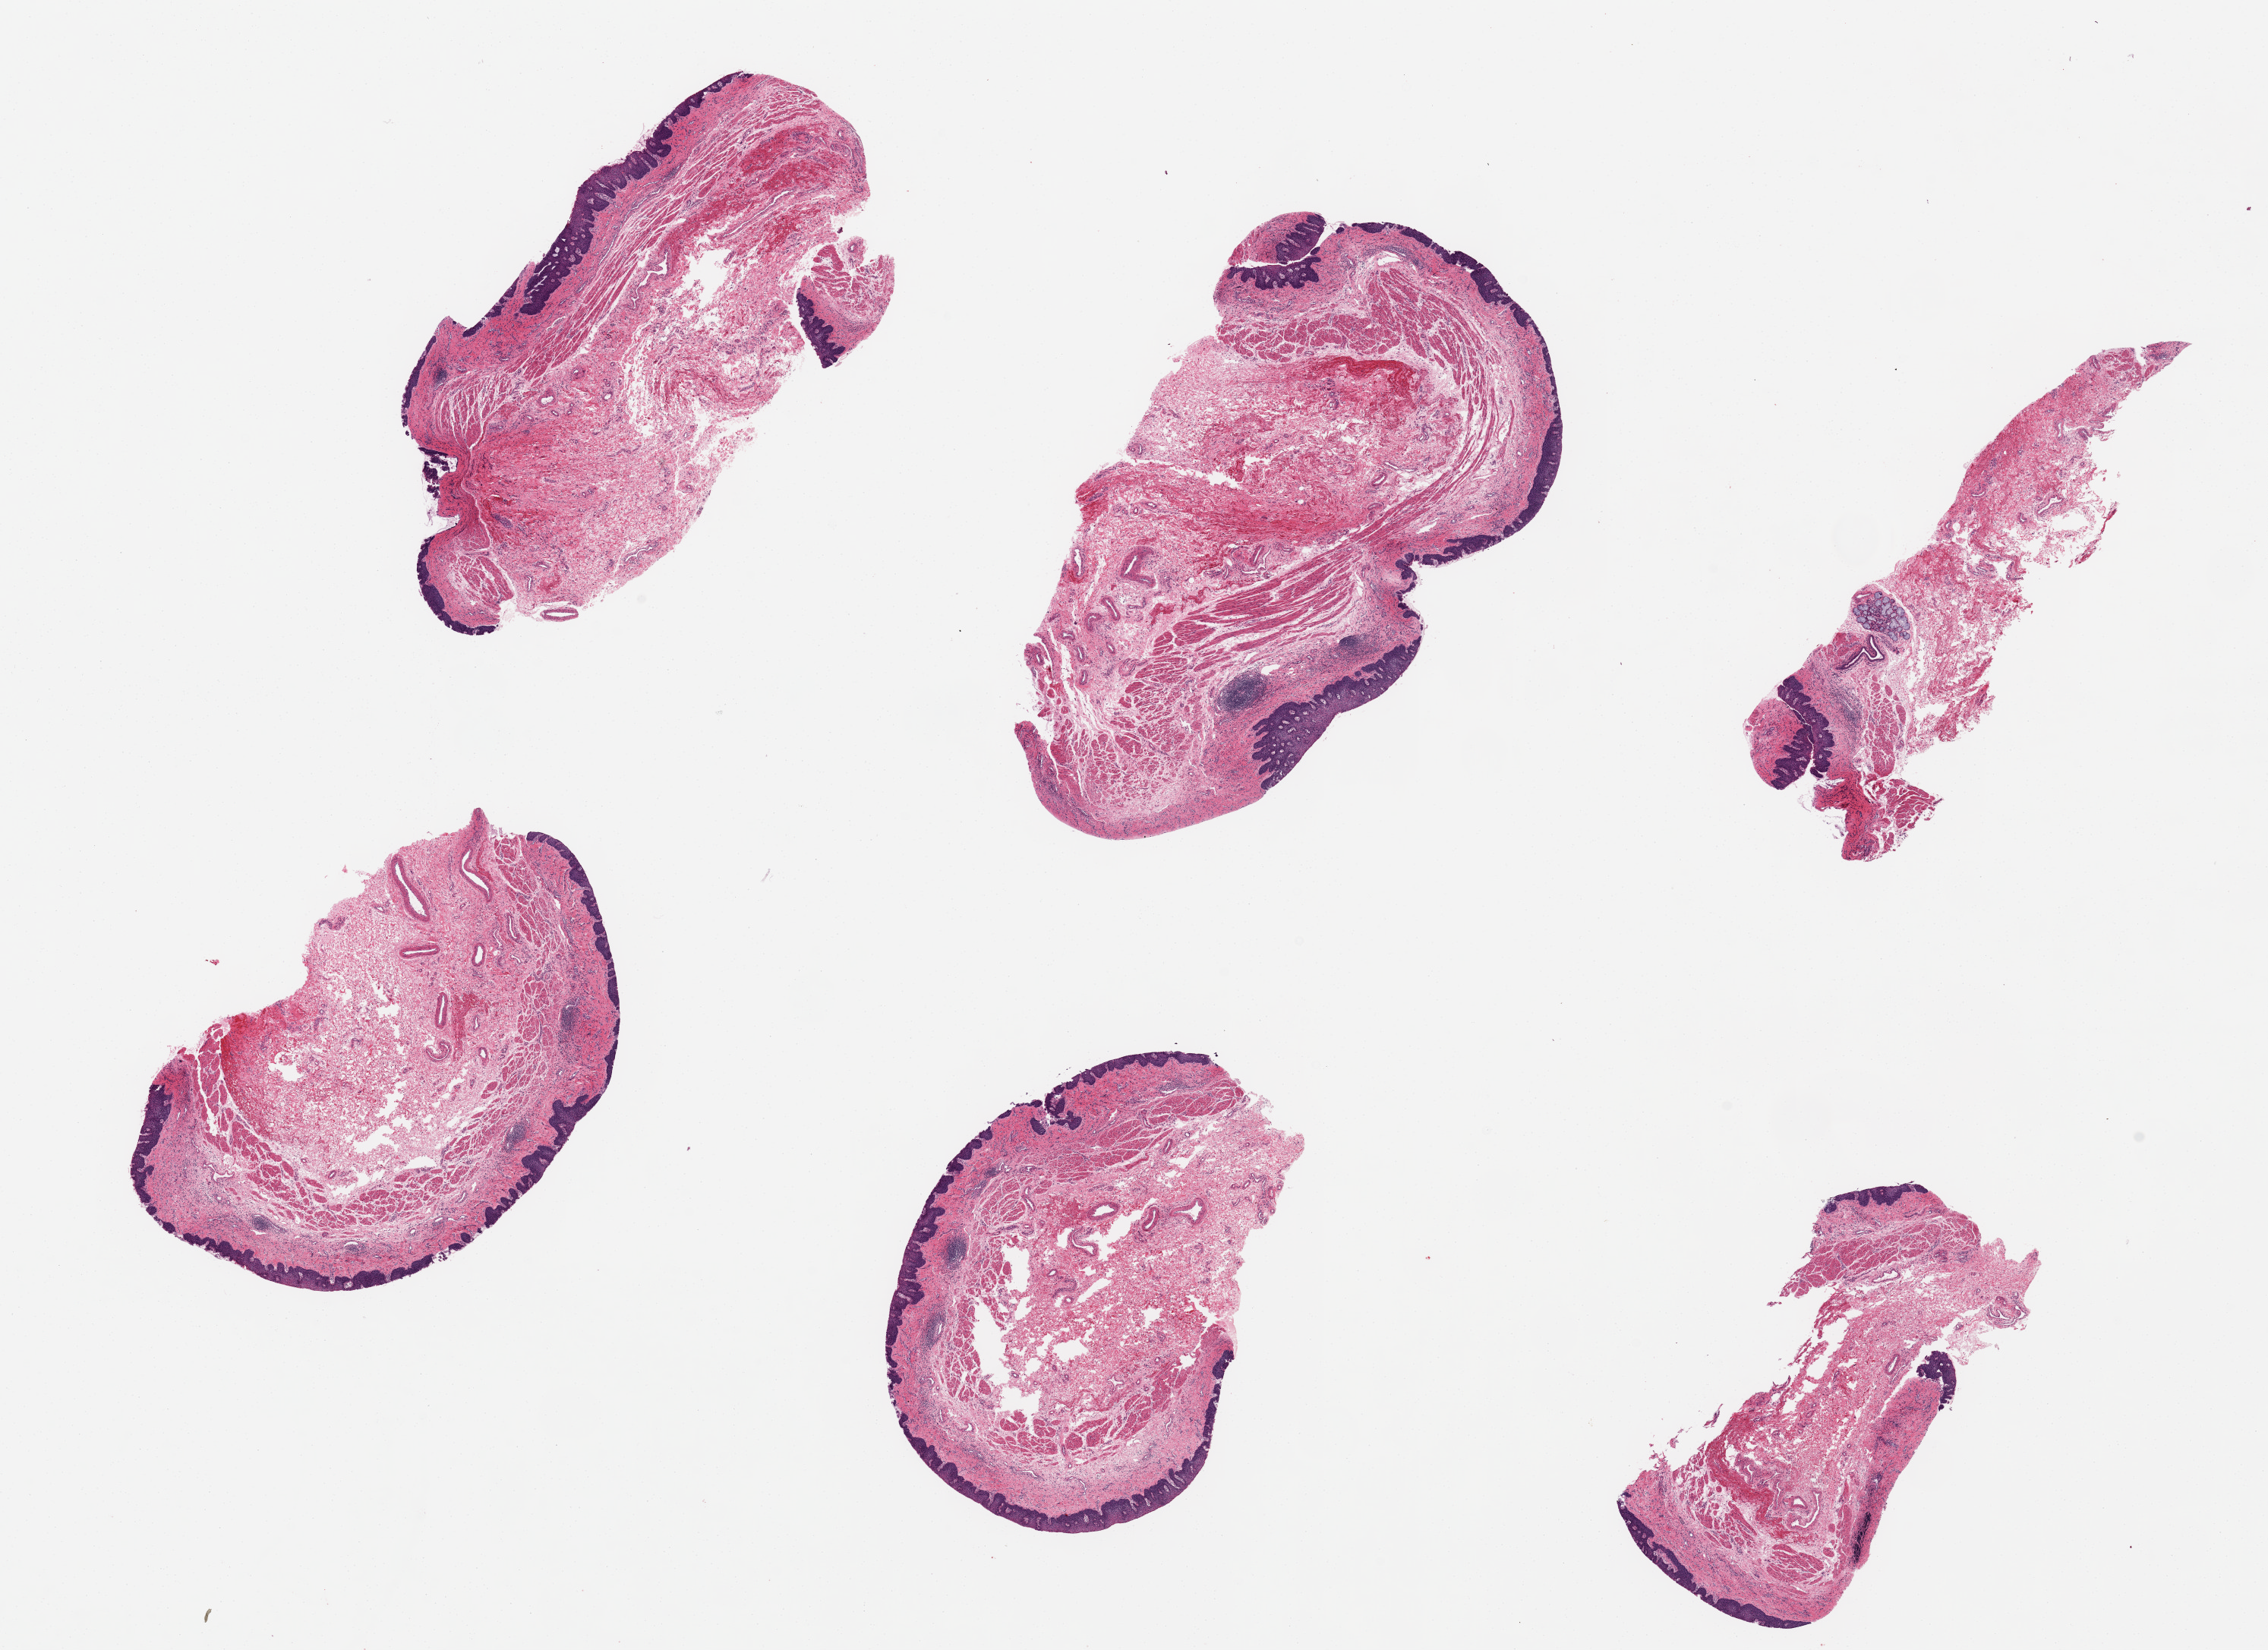
Whole-slide image, H&E stain, brightfield — a low-resolution overview of the entire scanned area, about 23.6 x 17.2 mm. PAXgene-fixed paraffin-embedded (PFPE) section. Sampled site (target tissue): esophageal mucous membrane. Tissue donor sample. Donor: male.
Reviewer comment on this tissue sample: 6 pieces, ~7x3mm. Squamous mucosa well preserved, ~5-10% of thickness.